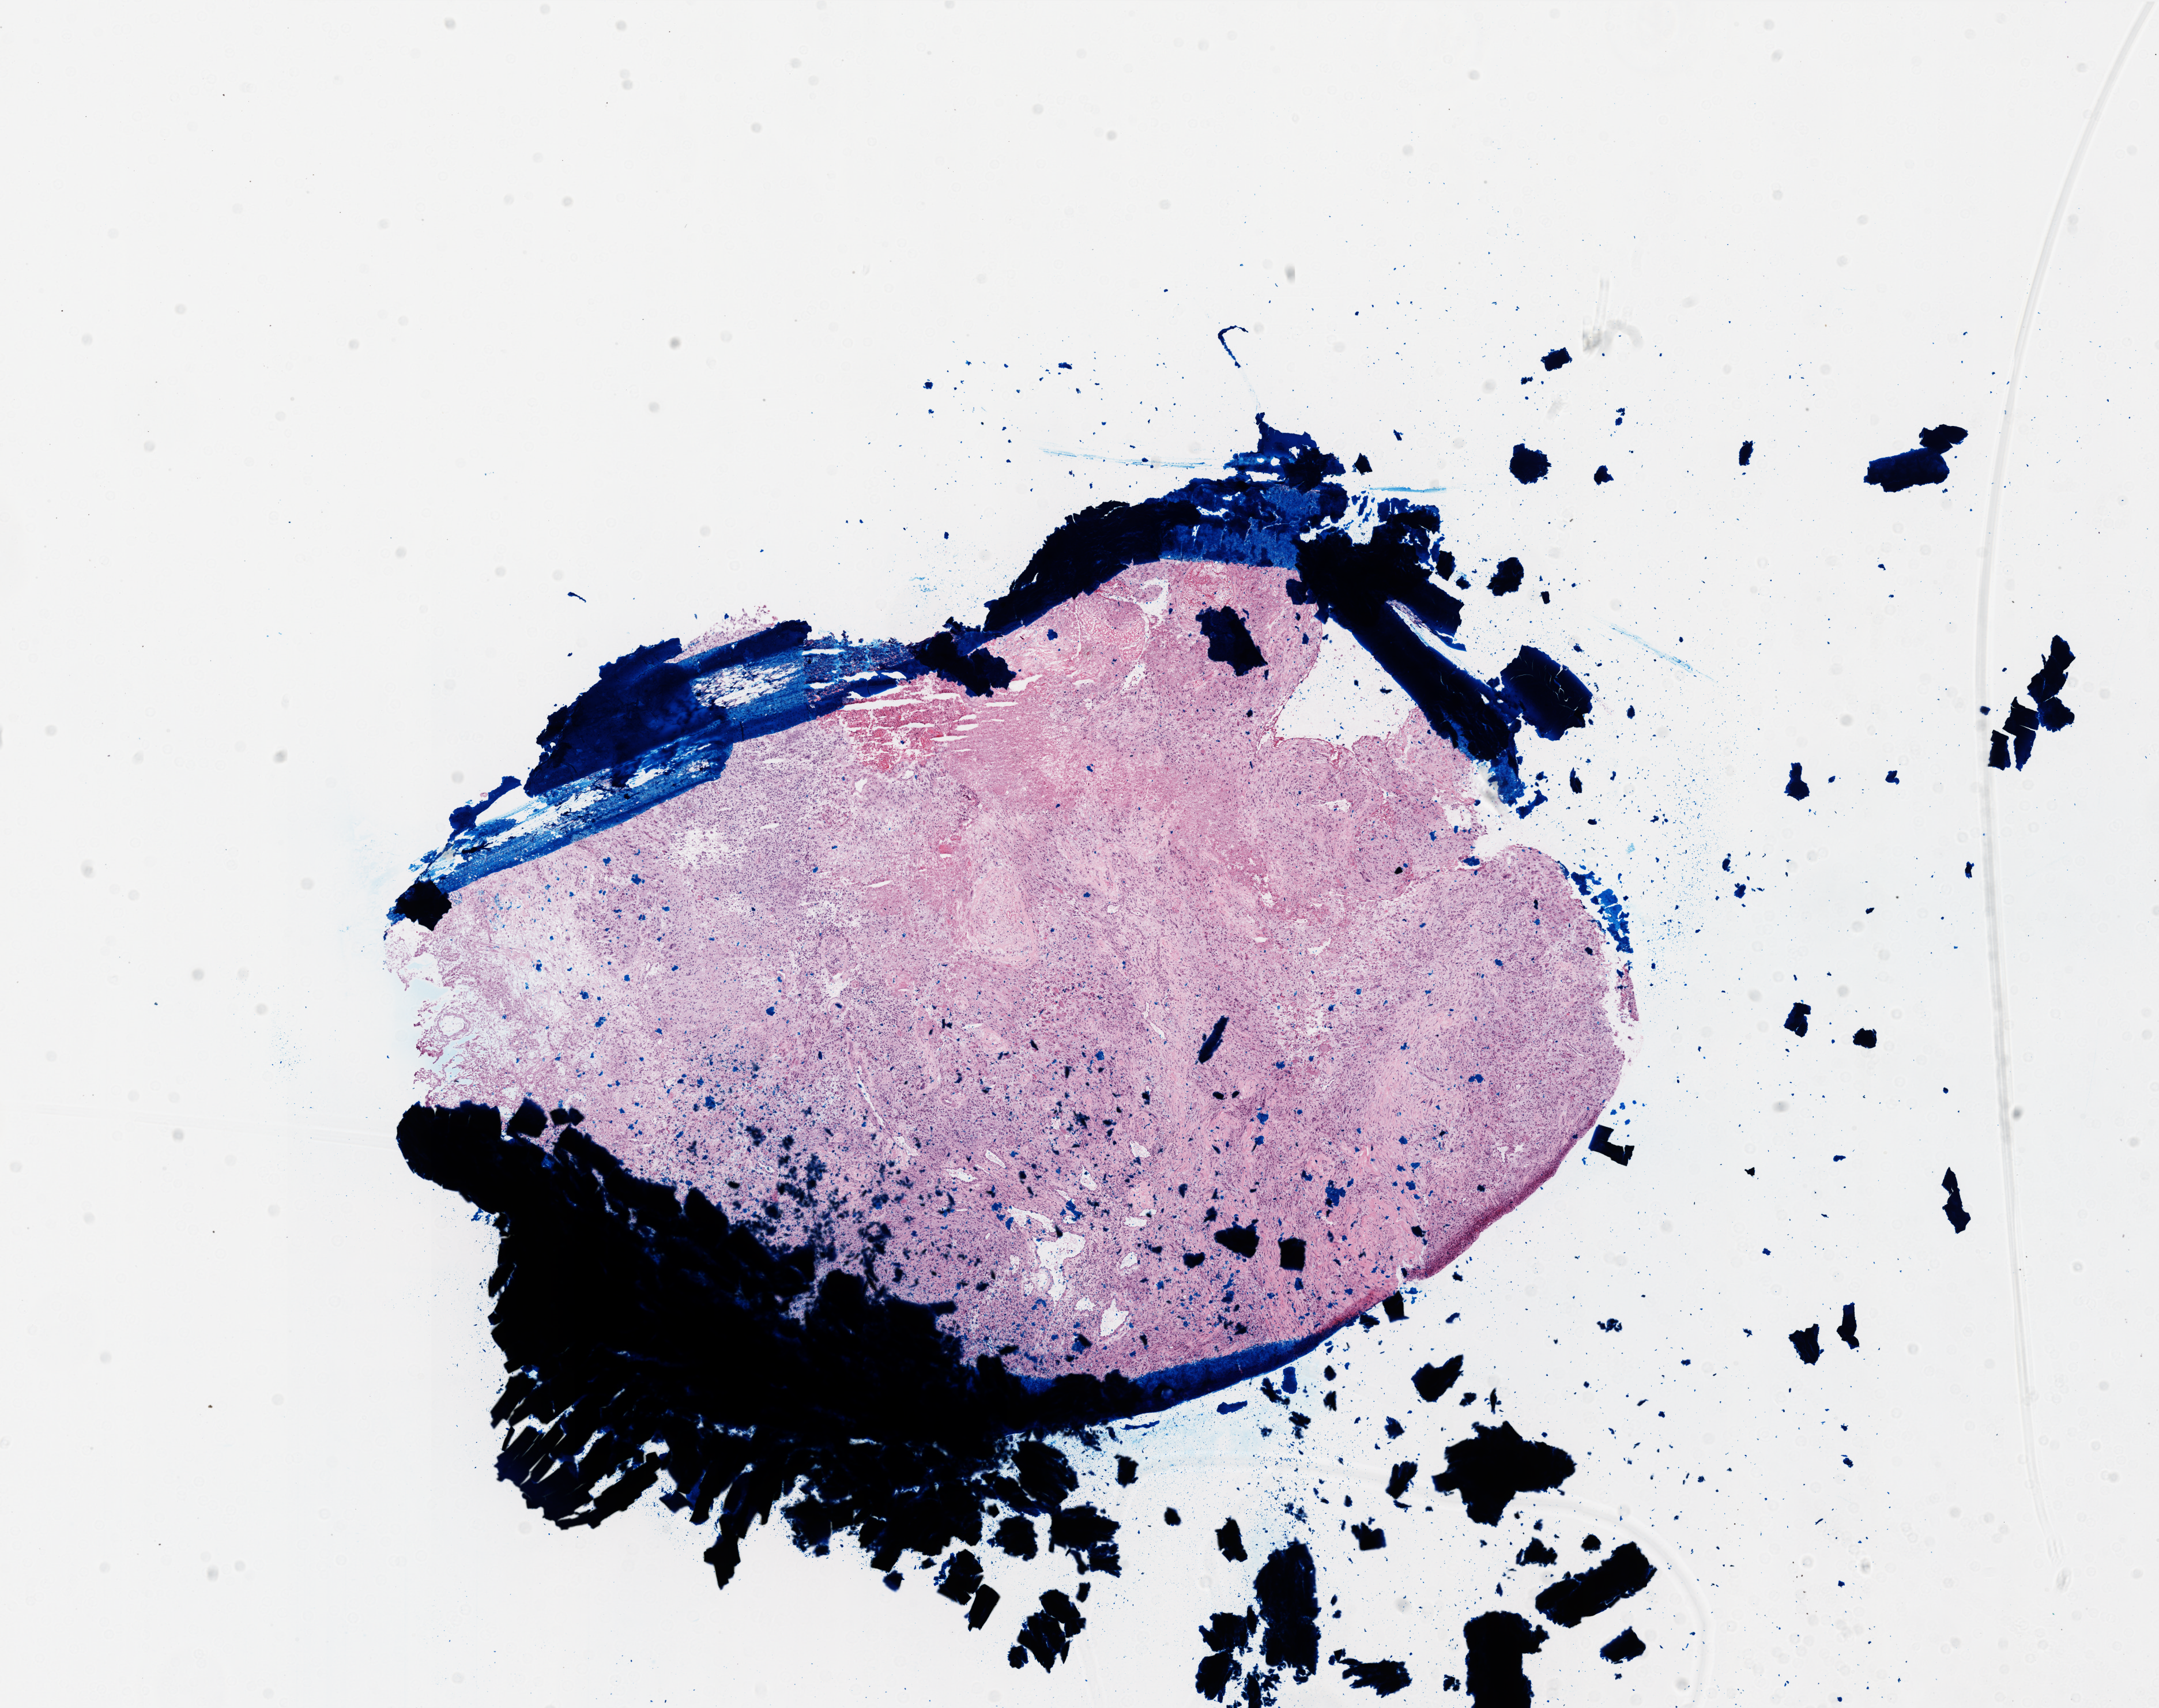
Digitized H&E tissue section (whole slide), low-resolution overview of the scanned area, about 15.0 x 11.9 mm (slide scanned at 20x). Frozen section from the top of the tissue portion. Sample: primary tumour, brain. Male patient; age at initial diagnosis 55 years. Composition of this section per pathologist review: tumour cells 75%, tumour nuclei 100%, normal cells 0%, stromal cells 0%, necrosis 25%.
Histologic diagnosis: Glioblastoma.